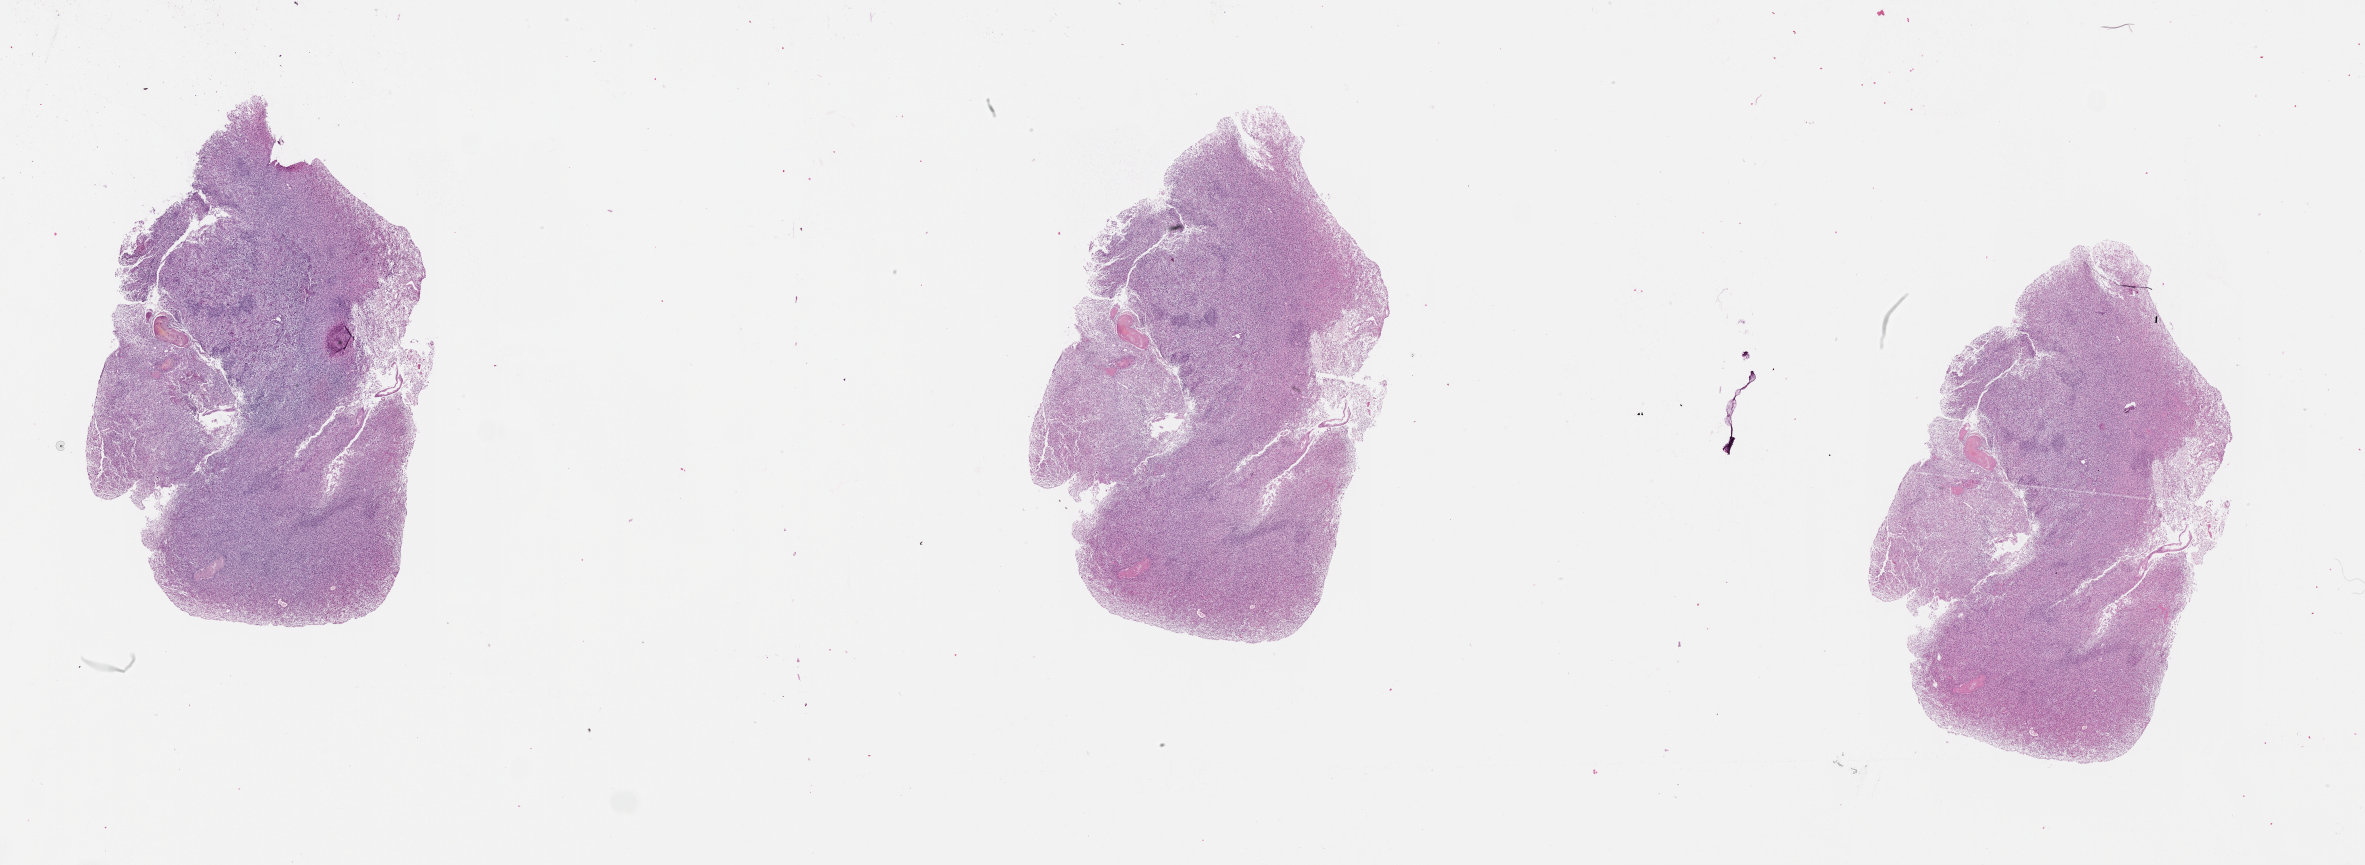
H&E whole-slide image, whole scanned area (about 38.1 x 13.9 mm, acquisition: 20x scan) shown as a low-resolution overview; brain, tumour tissue. 58-year-old male patient.
Primary tumour site (as recorded): frontal lobe. Diagnosis: Glioblastoma.